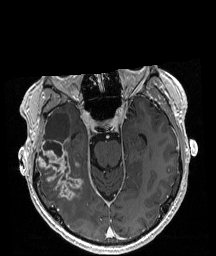
Brain MRI from a brain-tumour surgery series, one axial slice. Position 127 of 208 along the scan axis. T1-weighted post-contrast. 216 × 256 image matrix, field of view 211 × 250 mm. Case-level facts recorded for this patient, not image findings: histopathology: Astrocytoma; WHO grade: 4; IDH mutation: yes.
Annotated regions visible in this slice (outlined manually by an expert reader):
- tumour: box from (x=37, y=139) to (x=83, y=200) px